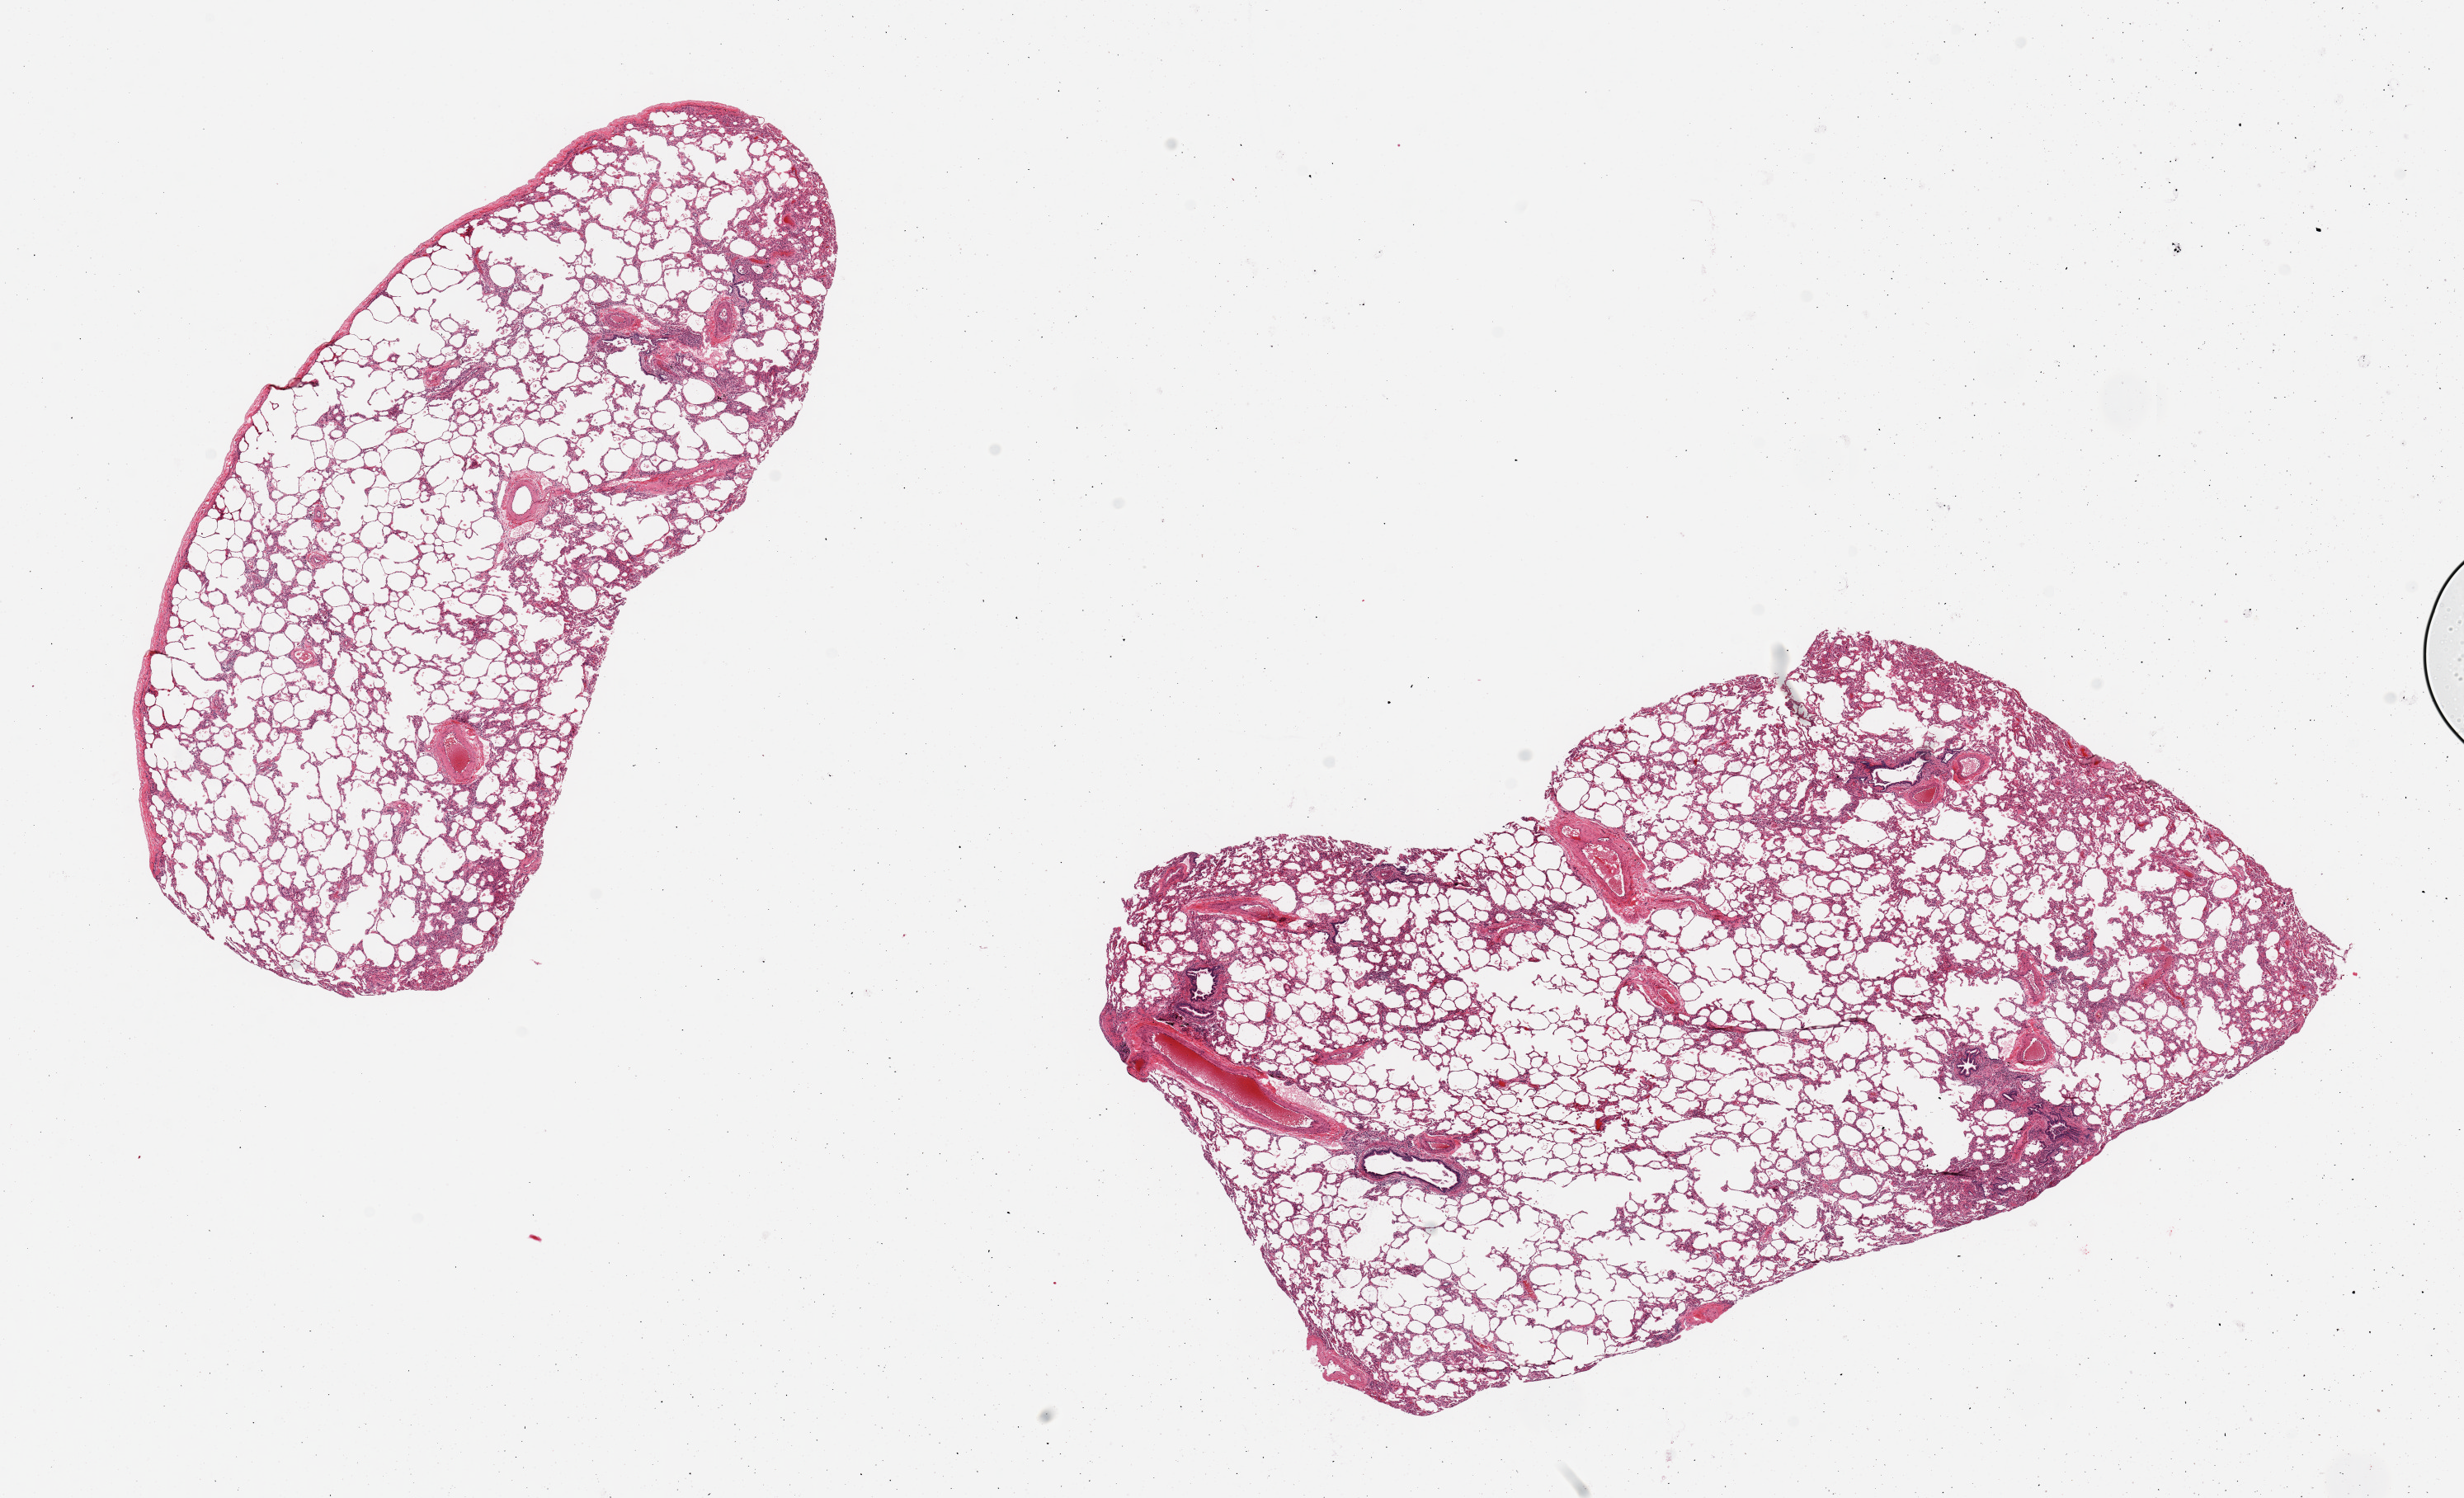
Whole-slide image, hematoxylin and eosin (H&E) stain, brightfield, shown as a low-resolution overview of the whole scanned area (about 23.6 x 14.4 mm), PAXgene-fixed paraffin-embedded (PFPE) section, sampled site (target tissue): lung, tissue donor sample. Female donor.
• reviewer comment on this tissue sample: 2 pieces, focal acute bronchitis/peribronchitis